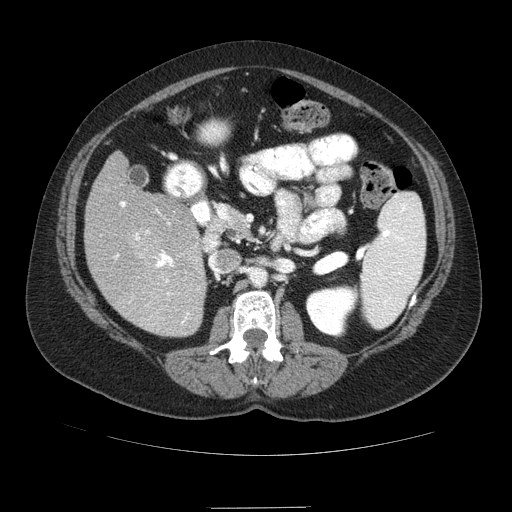
Contrast-enhanced abdominal CT (liver protocol), one axial slice; position 36 of 89 along the scan axis; reconstruction kernel STANDARD; soft-tissue window (W 400 / L 40 HU); 2.5 mm slice thickness; 512 × 512 image matrix, field of view 400 × 400 mm. From the clinical record (not read from this slice): diagnosis: hepatocellular carcinoma (patient treated with transarterial chemoembolisation; whether this scan precedes or follows treatment is not stated here); TNM stage (as recorded): Stage-IIIB; Child-Pugh class: A.
Structures marked on this image (semi-automatically segmented with operator editing):
- liver parenchyma outside the tumour (the mass and vessels are separate outlines, so this box may not span the whole liver): box from (x=84, y=152) to (x=206, y=336) px
- liver vessels: (x=114, y=201)–(x=190, y=324)